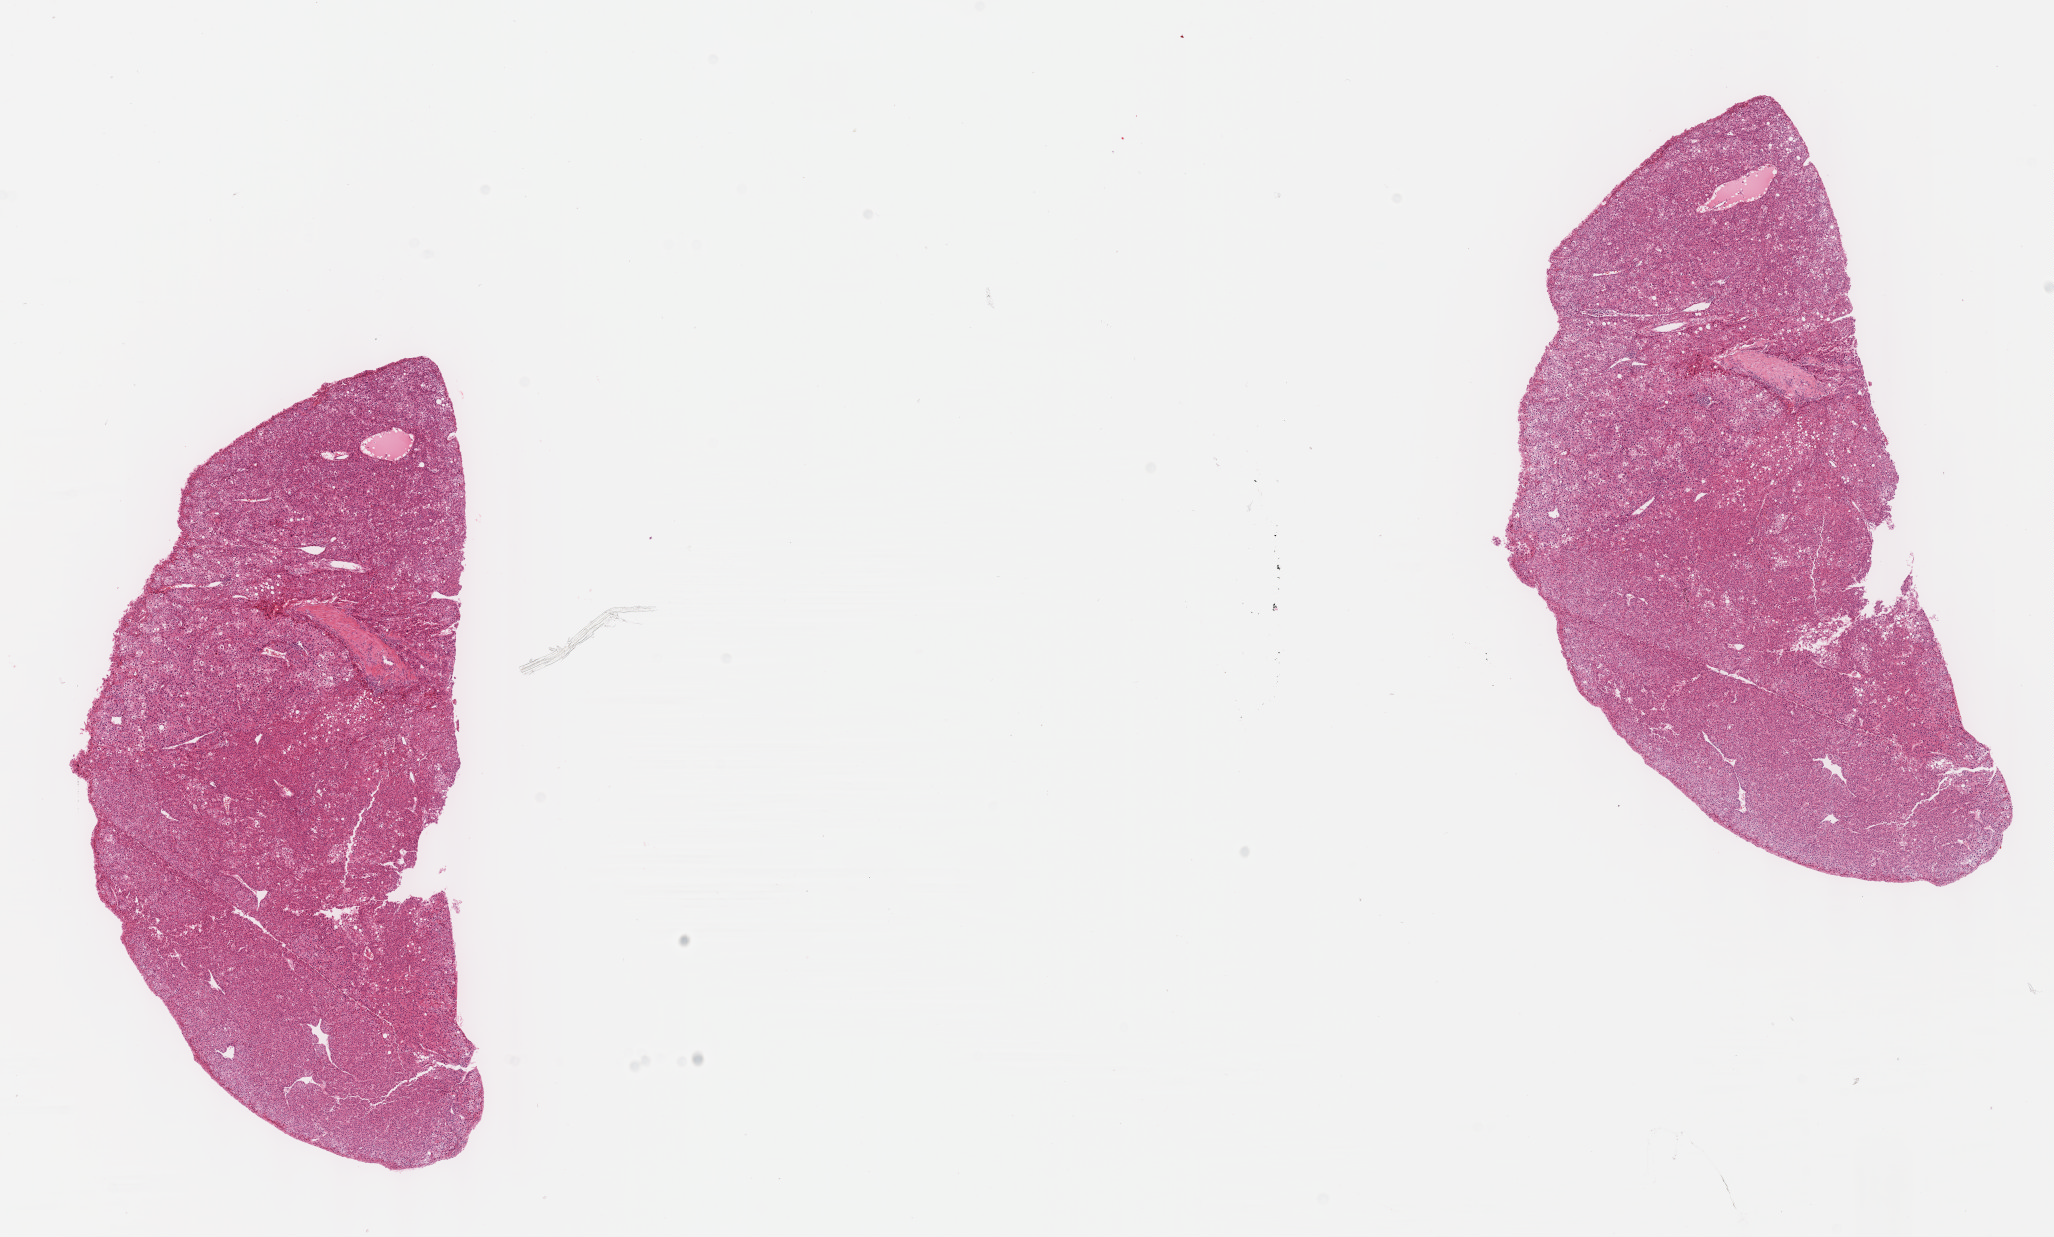
Digitized H&E tissue section (whole slide) — a low-resolution overview of the entire scanned area, about 16.6 x 10.0 mm (from a 40x scan). FFPE section. Sample: primary tumour, liver. Male patient; age at initial diagnosis 65 years. Histologic grade: G3 (poorly differentiated).
Histologic diagnosis: Hepatocellular carcinoma, NOS. AJCC pathologic stage: I.